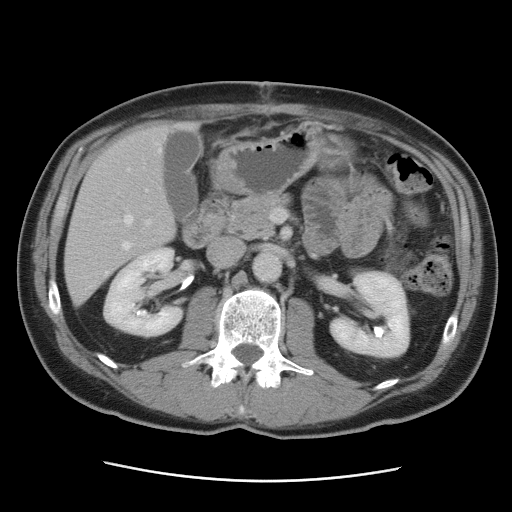
Contrast-enhanced abdominal CT, one axial slice; position 40 of 89 along the scan axis; 120 kVp; intravenous contrast given; soft-tissue window (W 400 / L 40 HU); 5 mm slice thickness; 512 × 512 image matrix, field of view 366 × 366 mm. Male patient, age 59 years. From the clinical record (not read from this slice): diagnosis: colorectal cancer liver metastases, imaged before liver resection; multiple liver metastases: yes; largest metastasis: 0.6 cm; chemotherapy before resection: no.
Annotated regions visible in this slice (expert manual segmentation):
- hepatic veins: box from (x=105, y=143) to (x=162, y=275) px
- liver: (x=65, y=122)–(x=196, y=305)
- planned liver remnant (the part of the liver to remain after resection): (x=73, y=123)–(x=198, y=245)
- portal vein (with intrahepatic branches): (x=145, y=189)–(x=151, y=225)